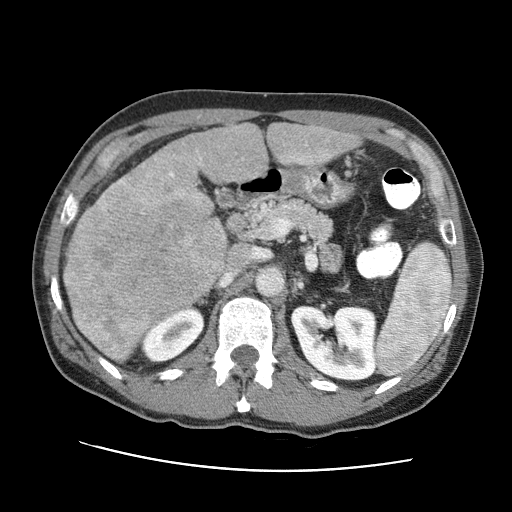
Contrast-enhanced abdominal CT (liver protocol), one axial slice. Position 40 of 95 along the scan axis. 120 kVp. One of 2 acquisitions stored at this slice position. Soft-tissue window (W 400 / L 40 HU). 512 × 512 image matrix. Case-level facts recorded for this patient, not image findings: diagnosis: hepatocellular carcinoma (patient treated with transarterial chemoembolisation; whether this scan precedes or follows treatment is not stated here); TNM stage (as recorded): Stage-IVA; Child-Pugh class: A; tumour nodularity: multinodular.
Annotated regions visible in this slice (semi-automatically segmented with operator editing):
- liver parenchyma outside the tumour (the mass and vessels are separate outlines, so this box may not span the whole liver): bounding box (x1, y1, x2, y2) in pixels: (62, 122, 358, 287)
- mass: (63, 161, 317, 364)
- liver vessels: (196, 143, 331, 165)